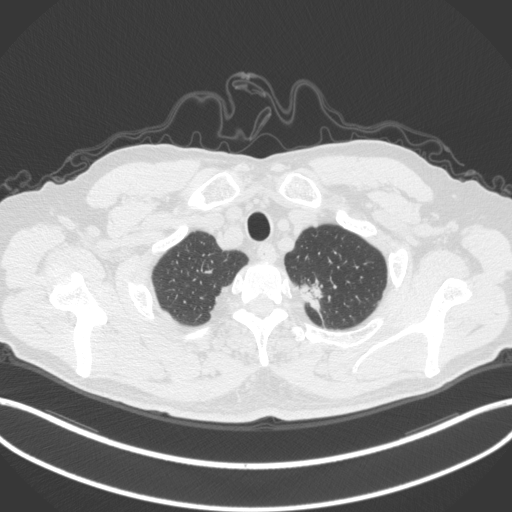
Chest CT, one axial slice; position 345 of 382 along the scan axis; reconstruction kernel B31f; lung window (W 1500 / L -600 HU); 1 mm slice thickness; 512 × 512 image matrix, field of view 400 × 400 mm. Male patient, age 64 years. From the clinical record (not read from this slice): clinical TNM (as recorded): T1c N0 M0.
Structures marked on this image (rectangle marked by the reading radiologist):
- lung tumour (recorded histology: adenocarcinoma): box from (x=299, y=278) to (x=330, y=315) px